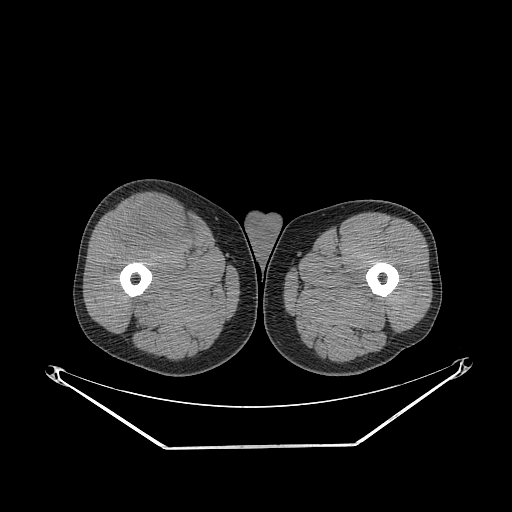
CT of an extremity soft-tissue mass (from a PET/CT study), one axial slice; soft-tissue window (W 400 / L 40 HU); 512 × 512 image matrix. Male patient. From the clinical record (not read from this slice): histological type: pleiomorphic leiomyosarcoma; grade: intermediate; site of the primary tumour: right thigh.
Structures marked on this image (expert contour drawn on MRI and transferred to this co-registered scan by the dataset authors):
- gross tumour volume including surrounding oedema: bounding box <117,201,188,254> (left, top, right, bottom; pixels)
- gross tumour volume (mass): <117,201,188,254>